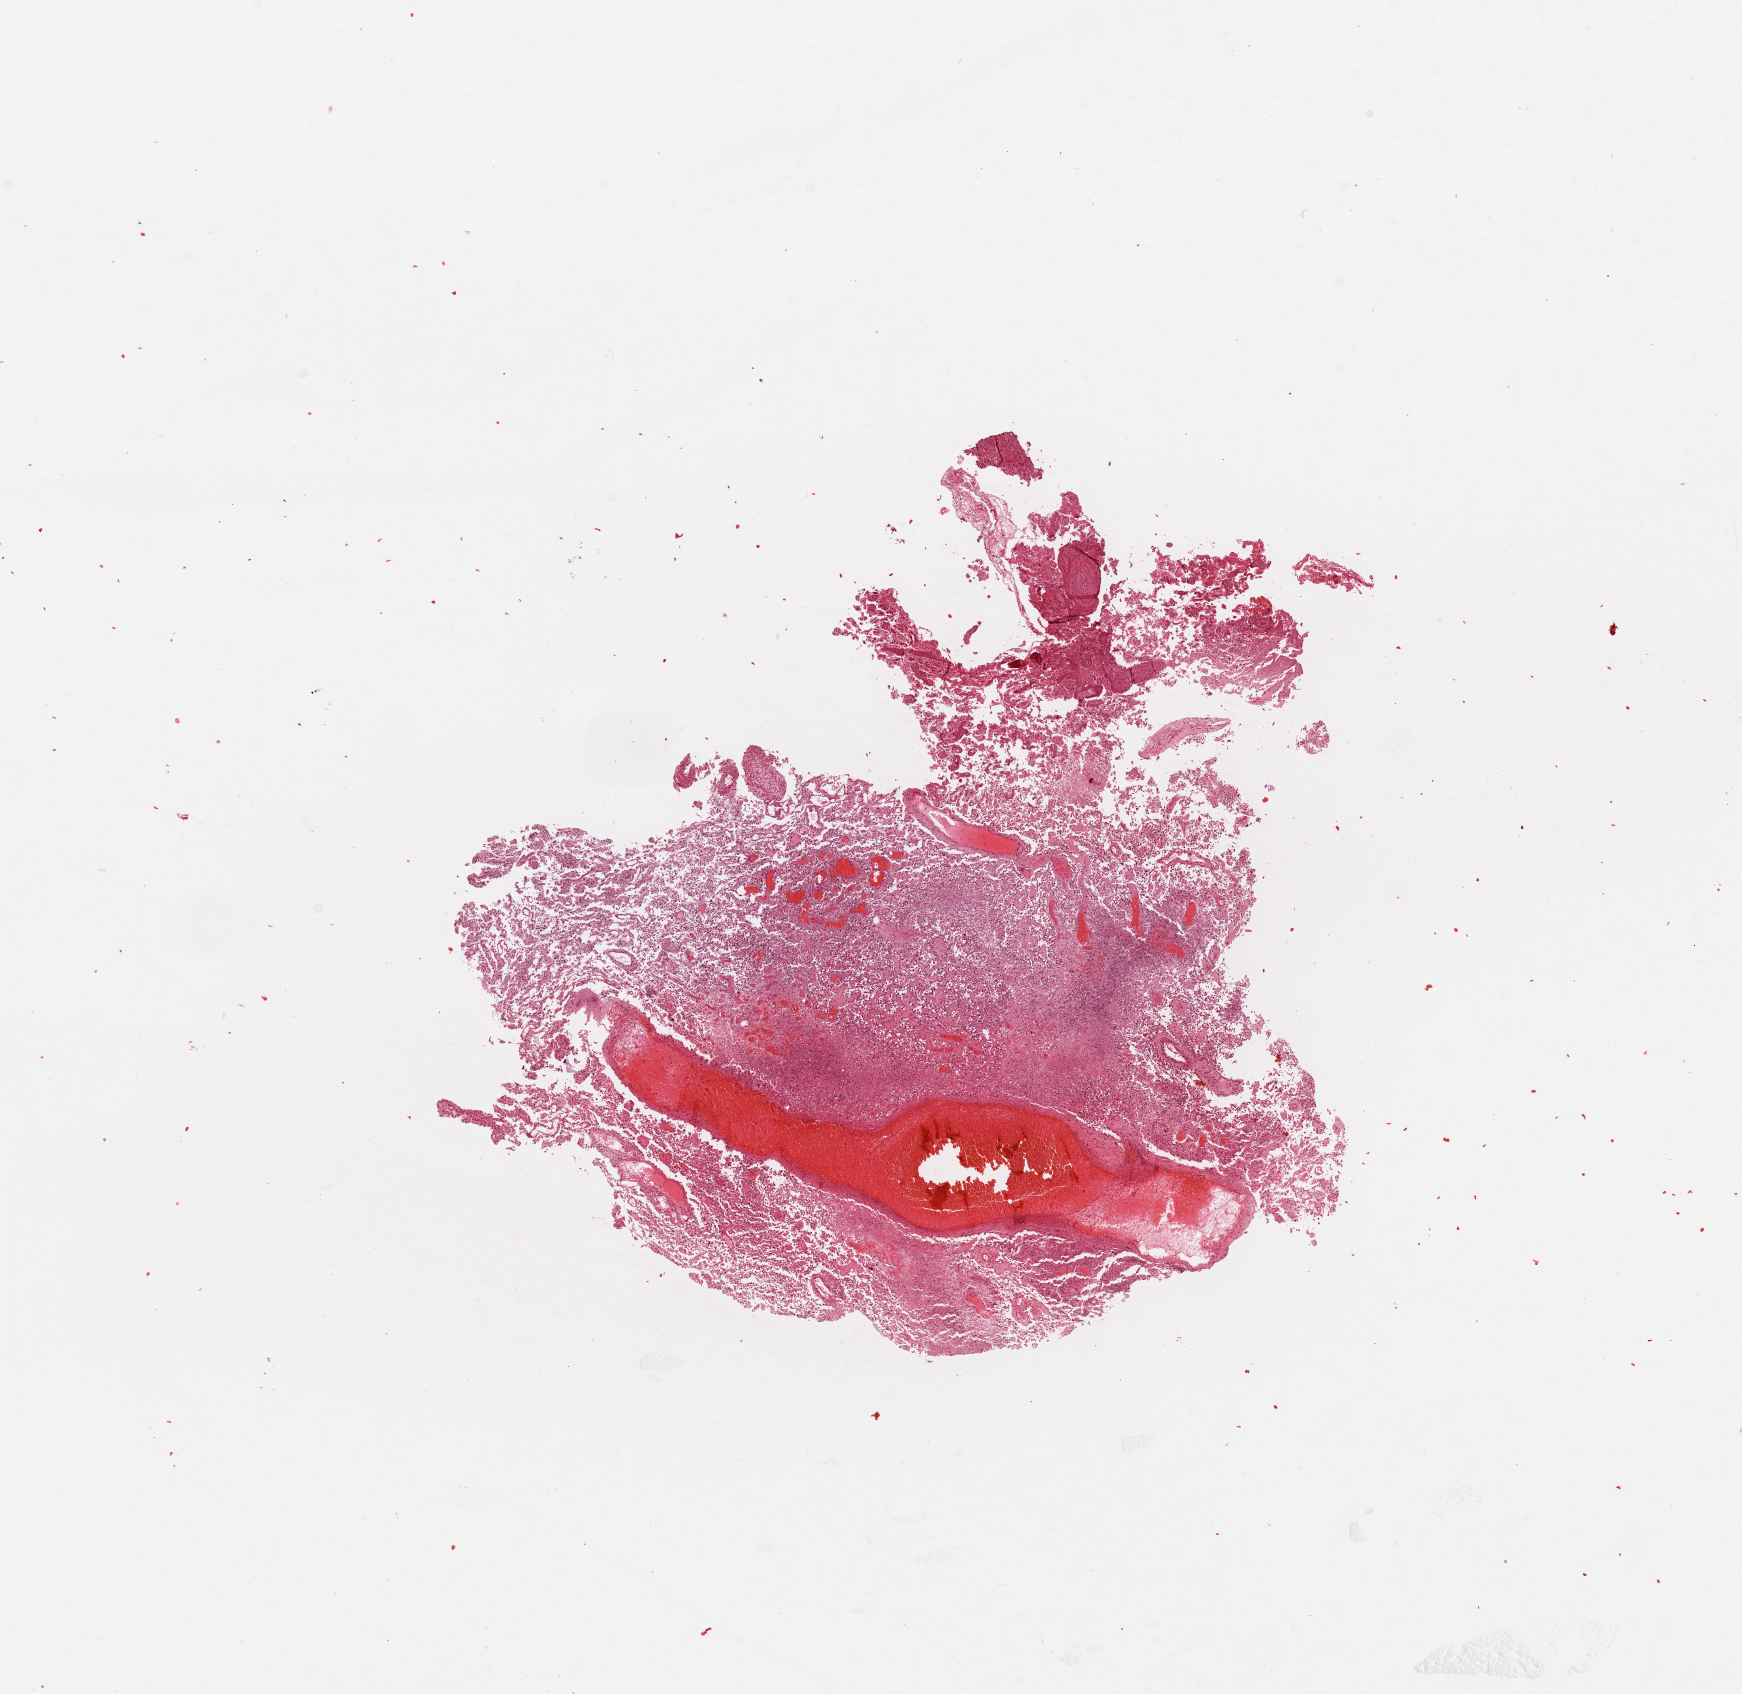
Digitized H&E tissue section (whole slide) — low-resolution overview of the scanned area, about 13.8 x 13.4 mm (acquisition: 20x scan), brain, tumour tissue. 71-year-old female patient.
Primary tumour site (as recorded): left hemisphere. Diagnosis: Glioblastoma.